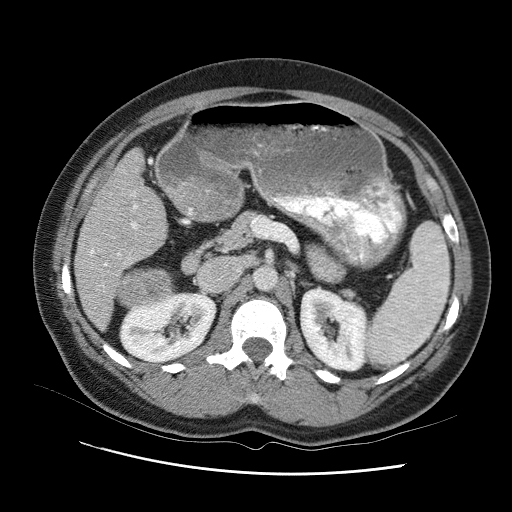
Contrast-enhanced abdominal CT (liver protocol), one axial slice. Slice 42 of 95 in the series (ordered by position). 120 kVp. One of 2 acquisitions stored at this slice position. Soft-tissue window (W 400 / L 40 HU). 2.5 mm slice thickness. 512 × 512 image matrix. From the clinical record (not read from this slice): diagnosis: hepatocellular carcinoma (patient treated with transarterial chemoembolisation; whether this scan precedes or follows treatment is not stated here); TNM stage (as recorded): Stage-I; Child-Pugh class: B.
Structures marked on this image (semi-automatic segmentation, software-assisted and operator-edited):
- liver parenchyma outside the tumour (the mass and vessels are separate outlines, so this box may not span the whole liver): box from (x=74, y=138) to (x=182, y=342) px
- mass: (x=112, y=250)–(x=183, y=309)
- liver vessels: (x=98, y=179)–(x=147, y=319)